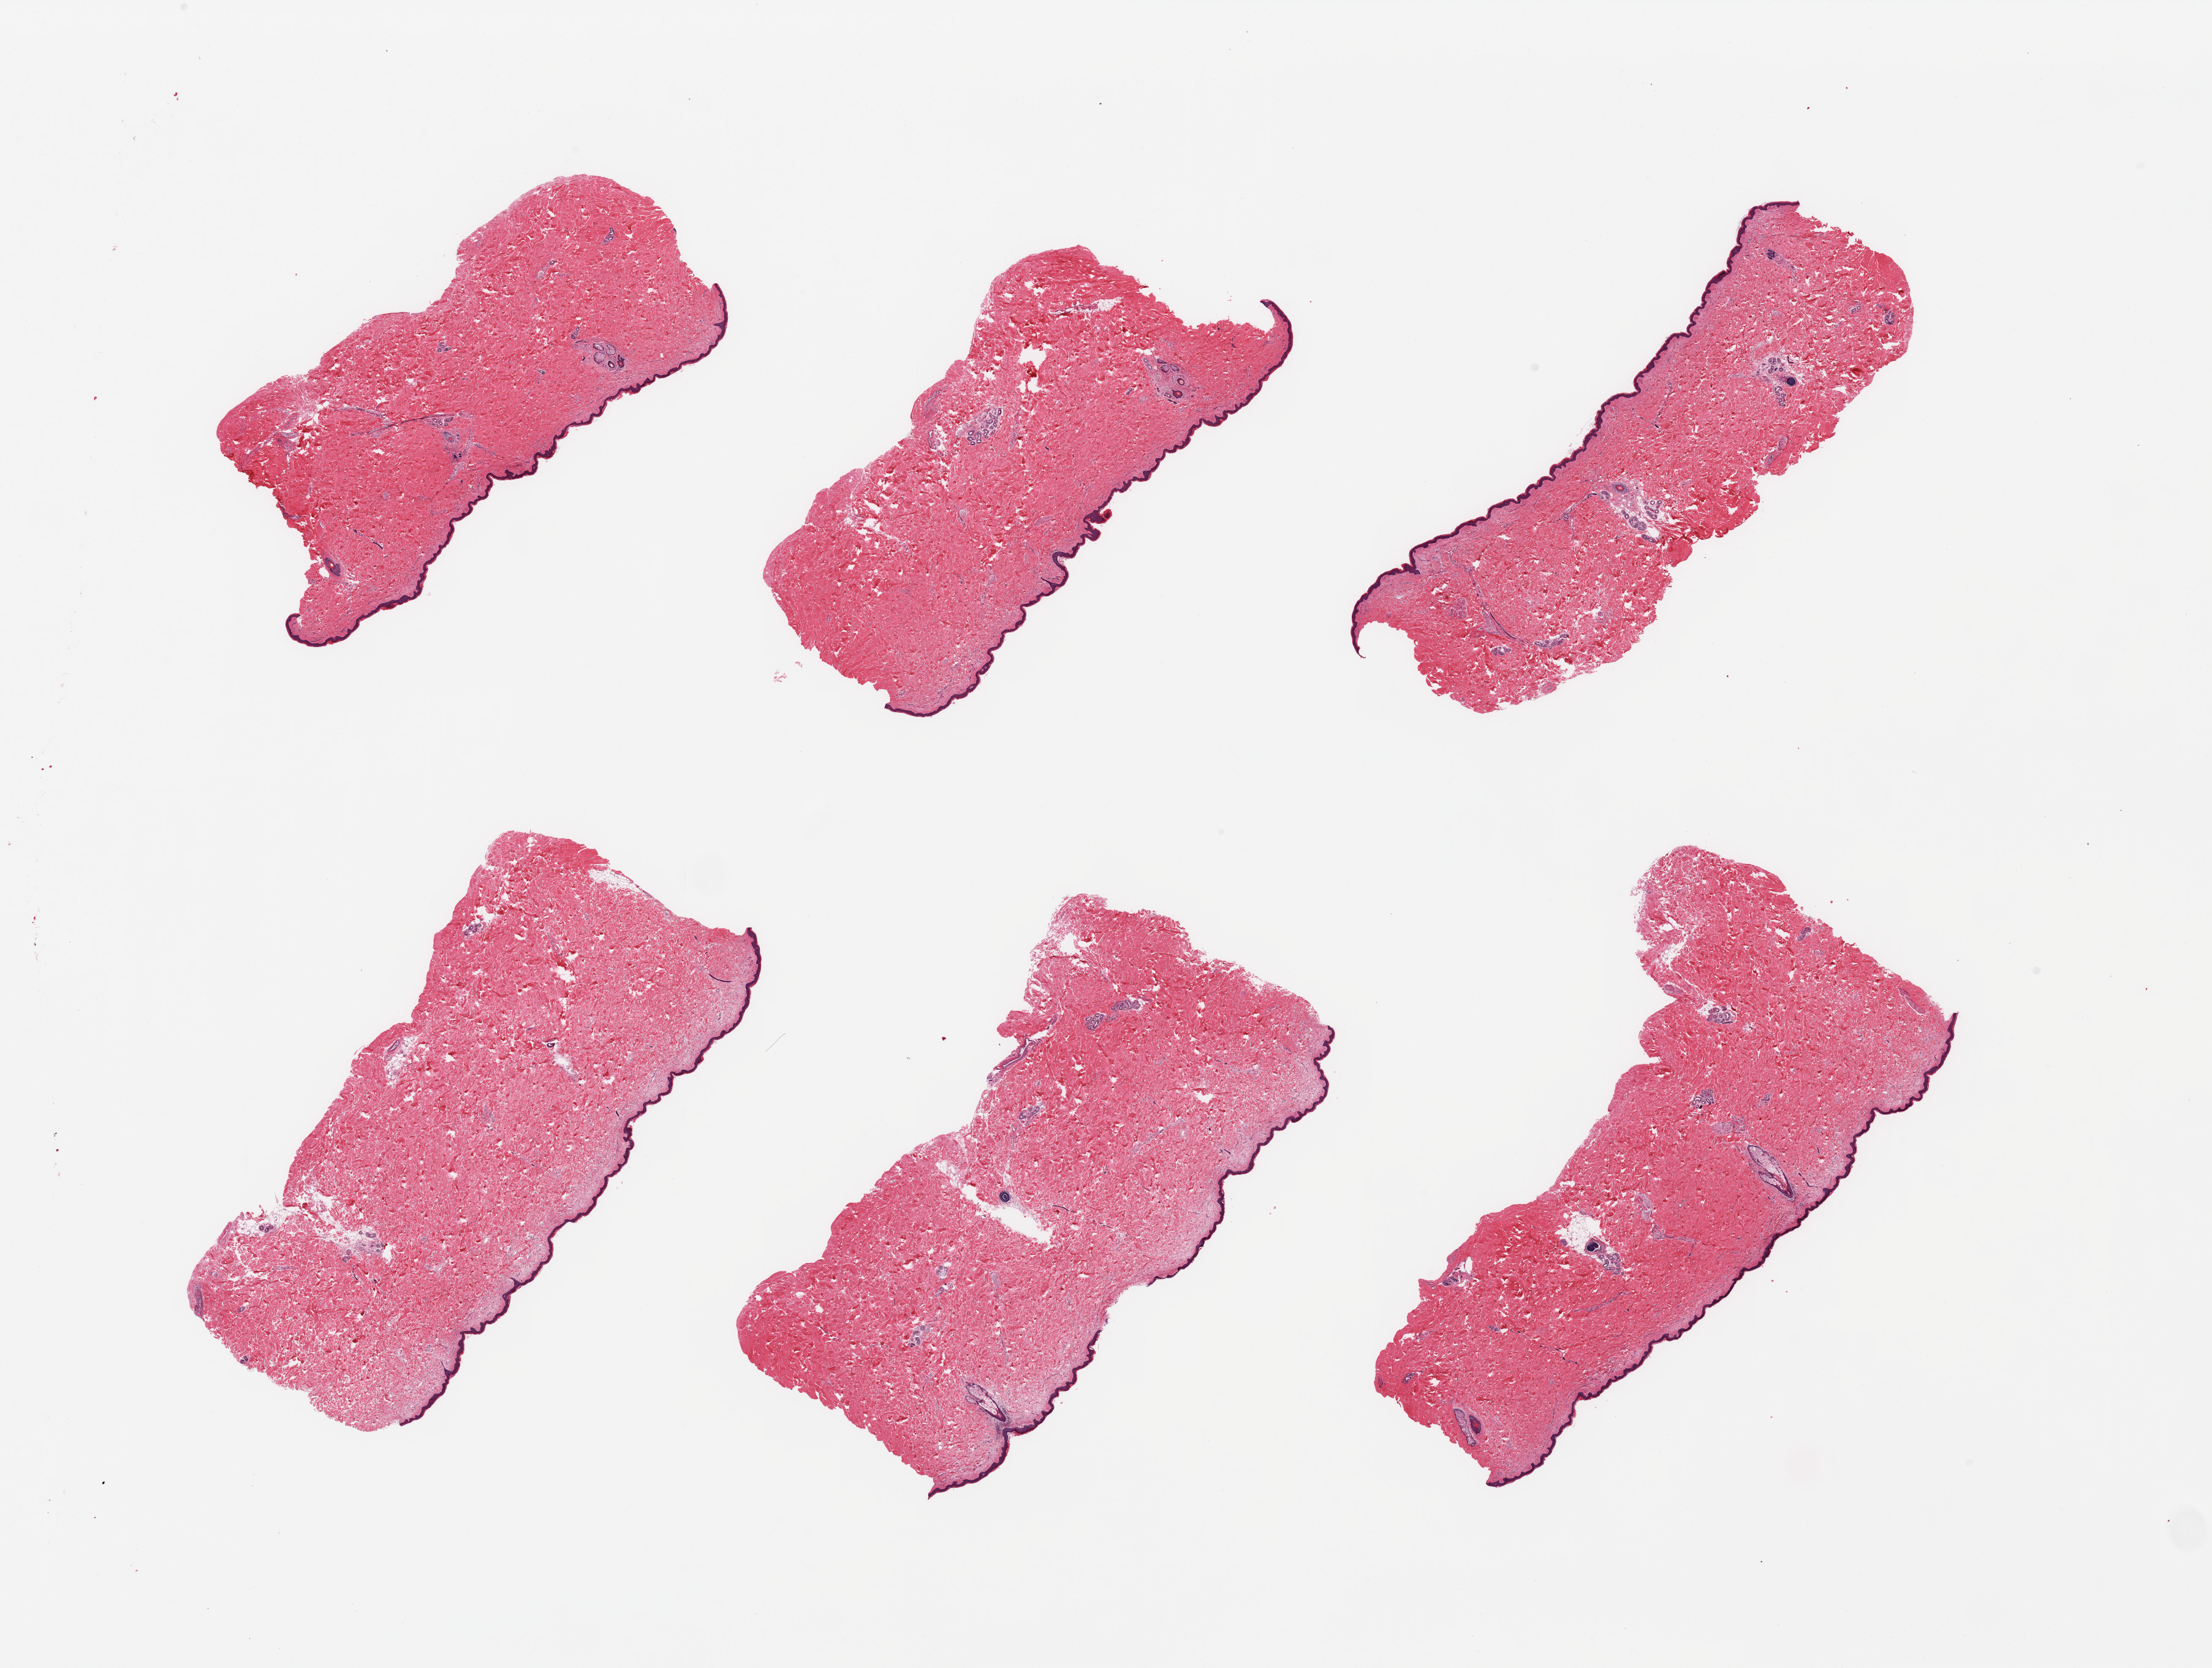
Digitized haematoxylin and eosin-stained section, shown as a low-resolution overview of the whole scanned area (about 28.5 x 21.5 mm); PAXgene-fixed, paraffin-embedded tissue; sampled site (target tissue): skin of suprapubic region; donor tissue sample. Donor sex: female.
- pathologist's review note for this sample: 6 pieces; well trimmed skin with a few hair follicles